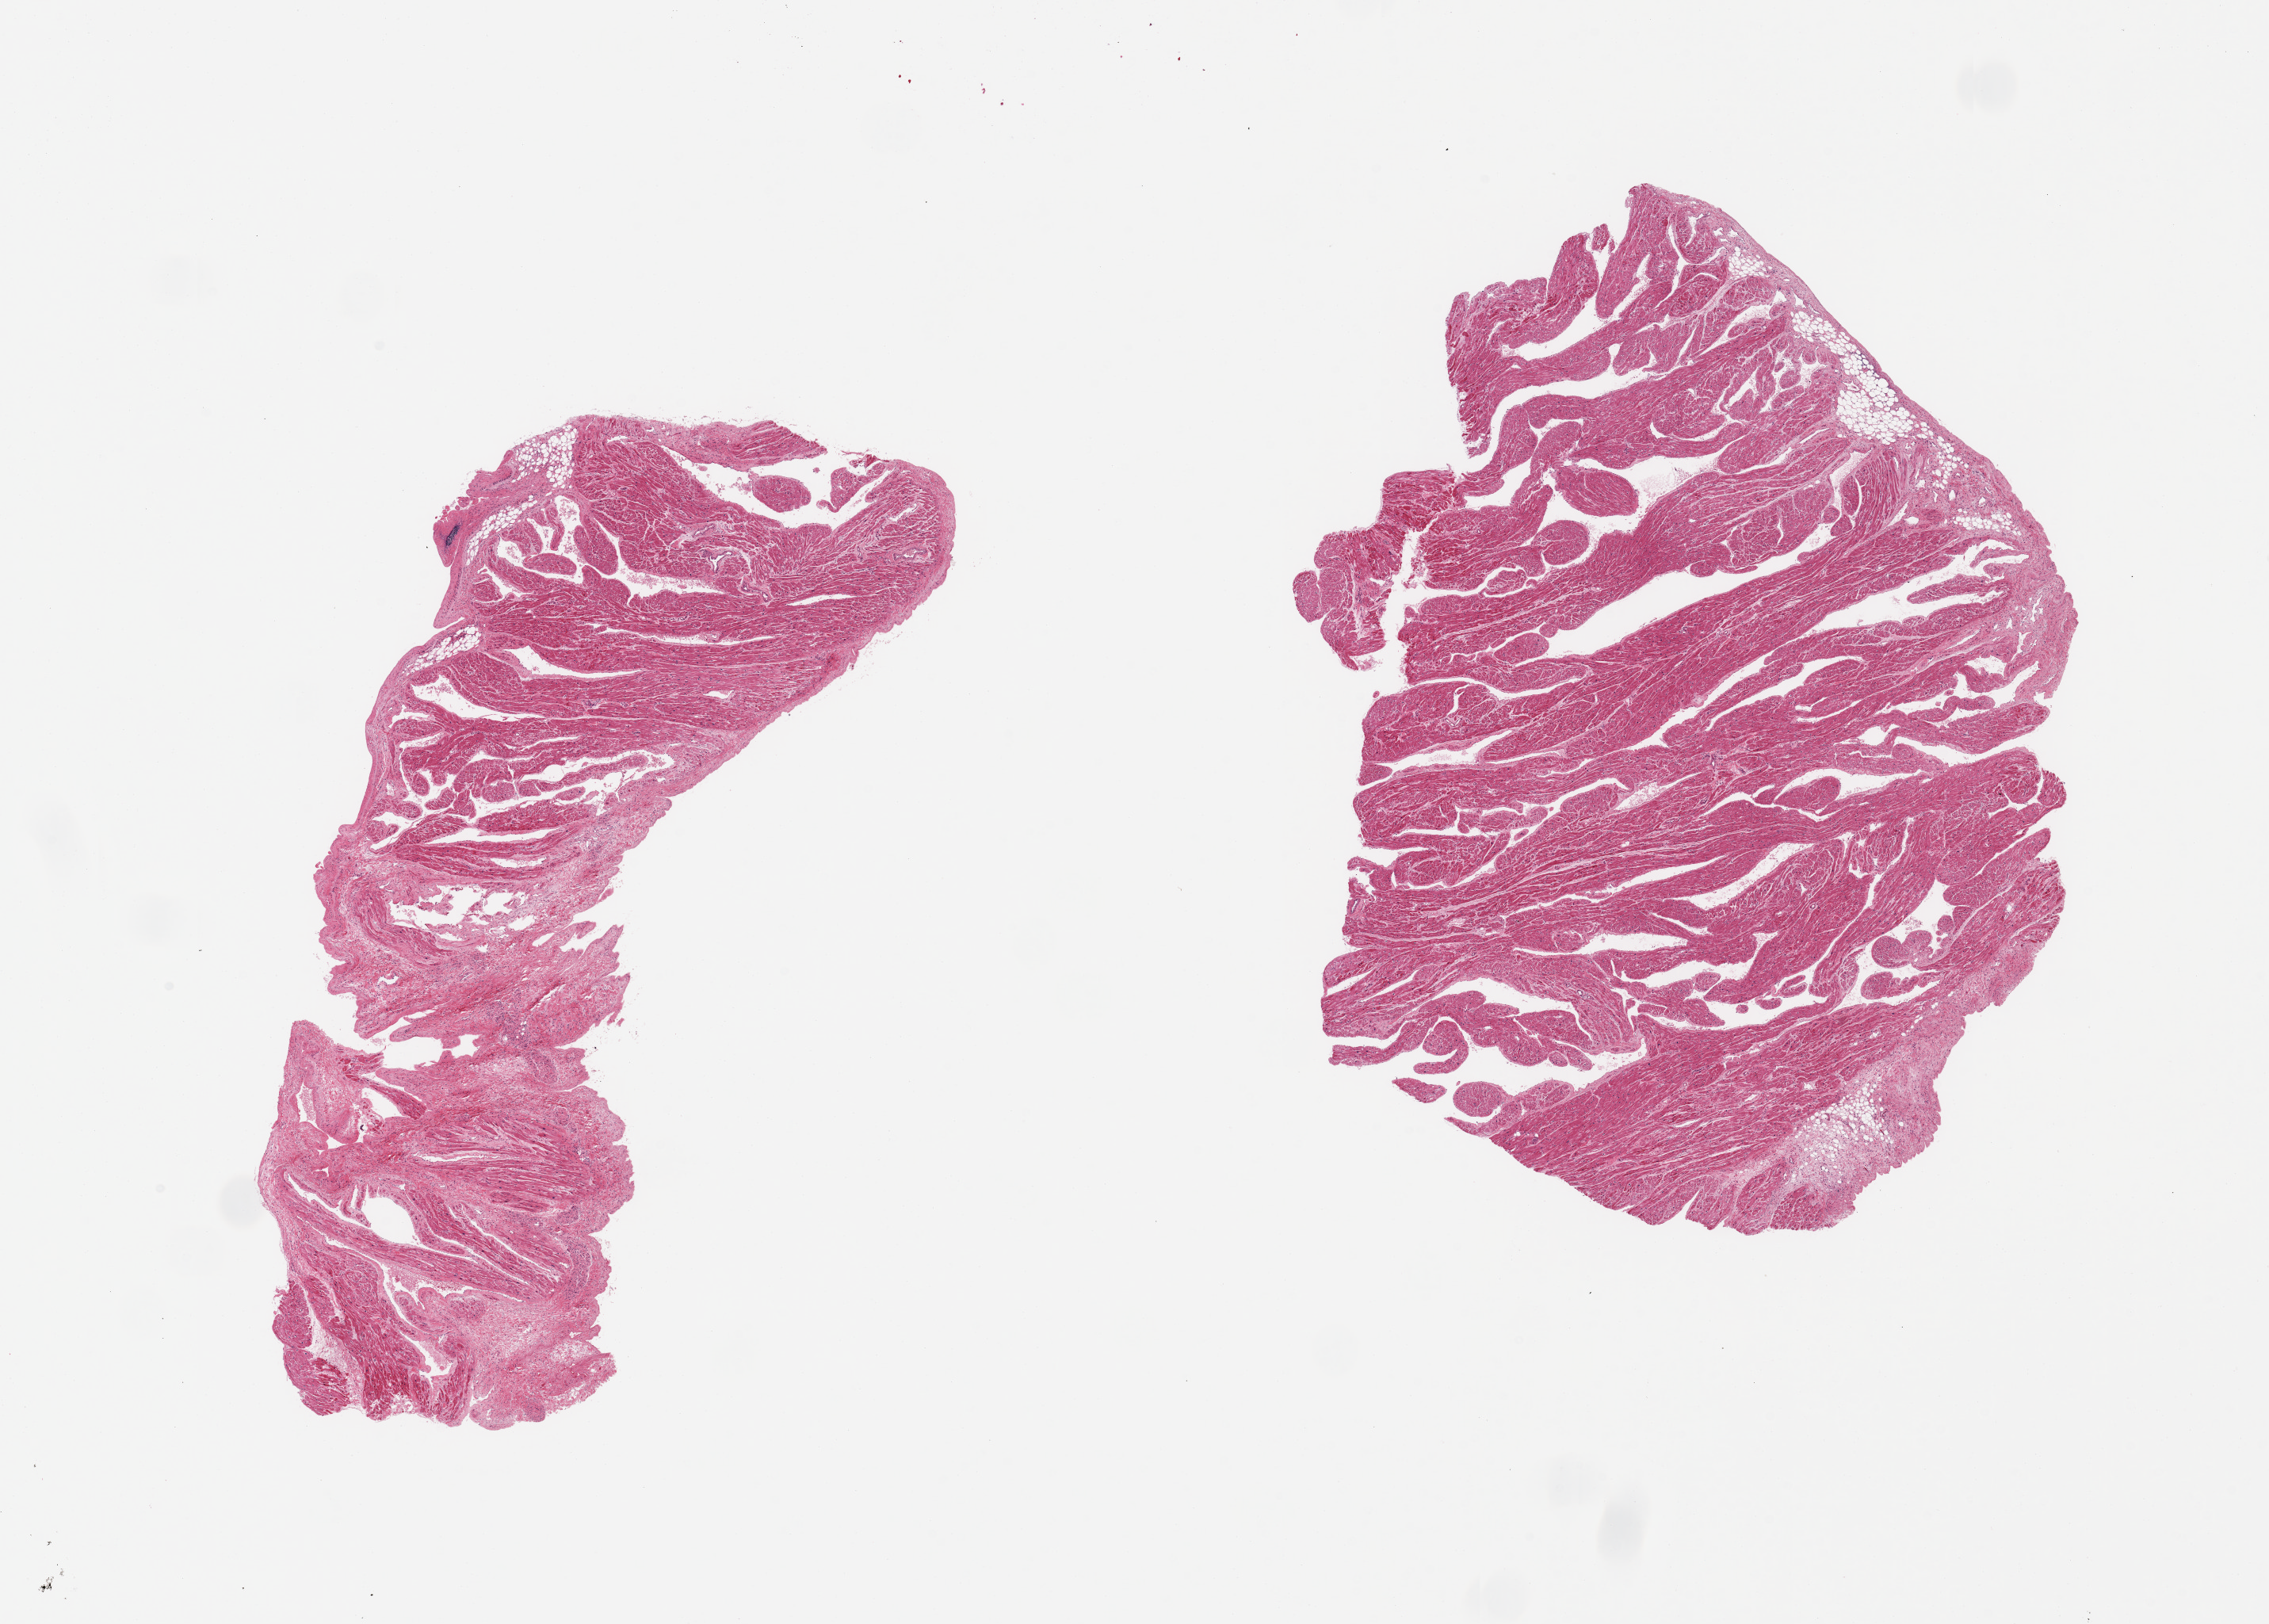
Haematoxylin and eosin whole-slide image, low-resolution overview of the scanned area, about 22.6 x 16.2 mm (acquisition: 20x scan); PAXgene-fixed paraffin-embedded (PFPE) section; sampled site (target tissue): auricular appendage; donor tissue sample.
Review note (as recorded): 2 pieces; minimal fat.